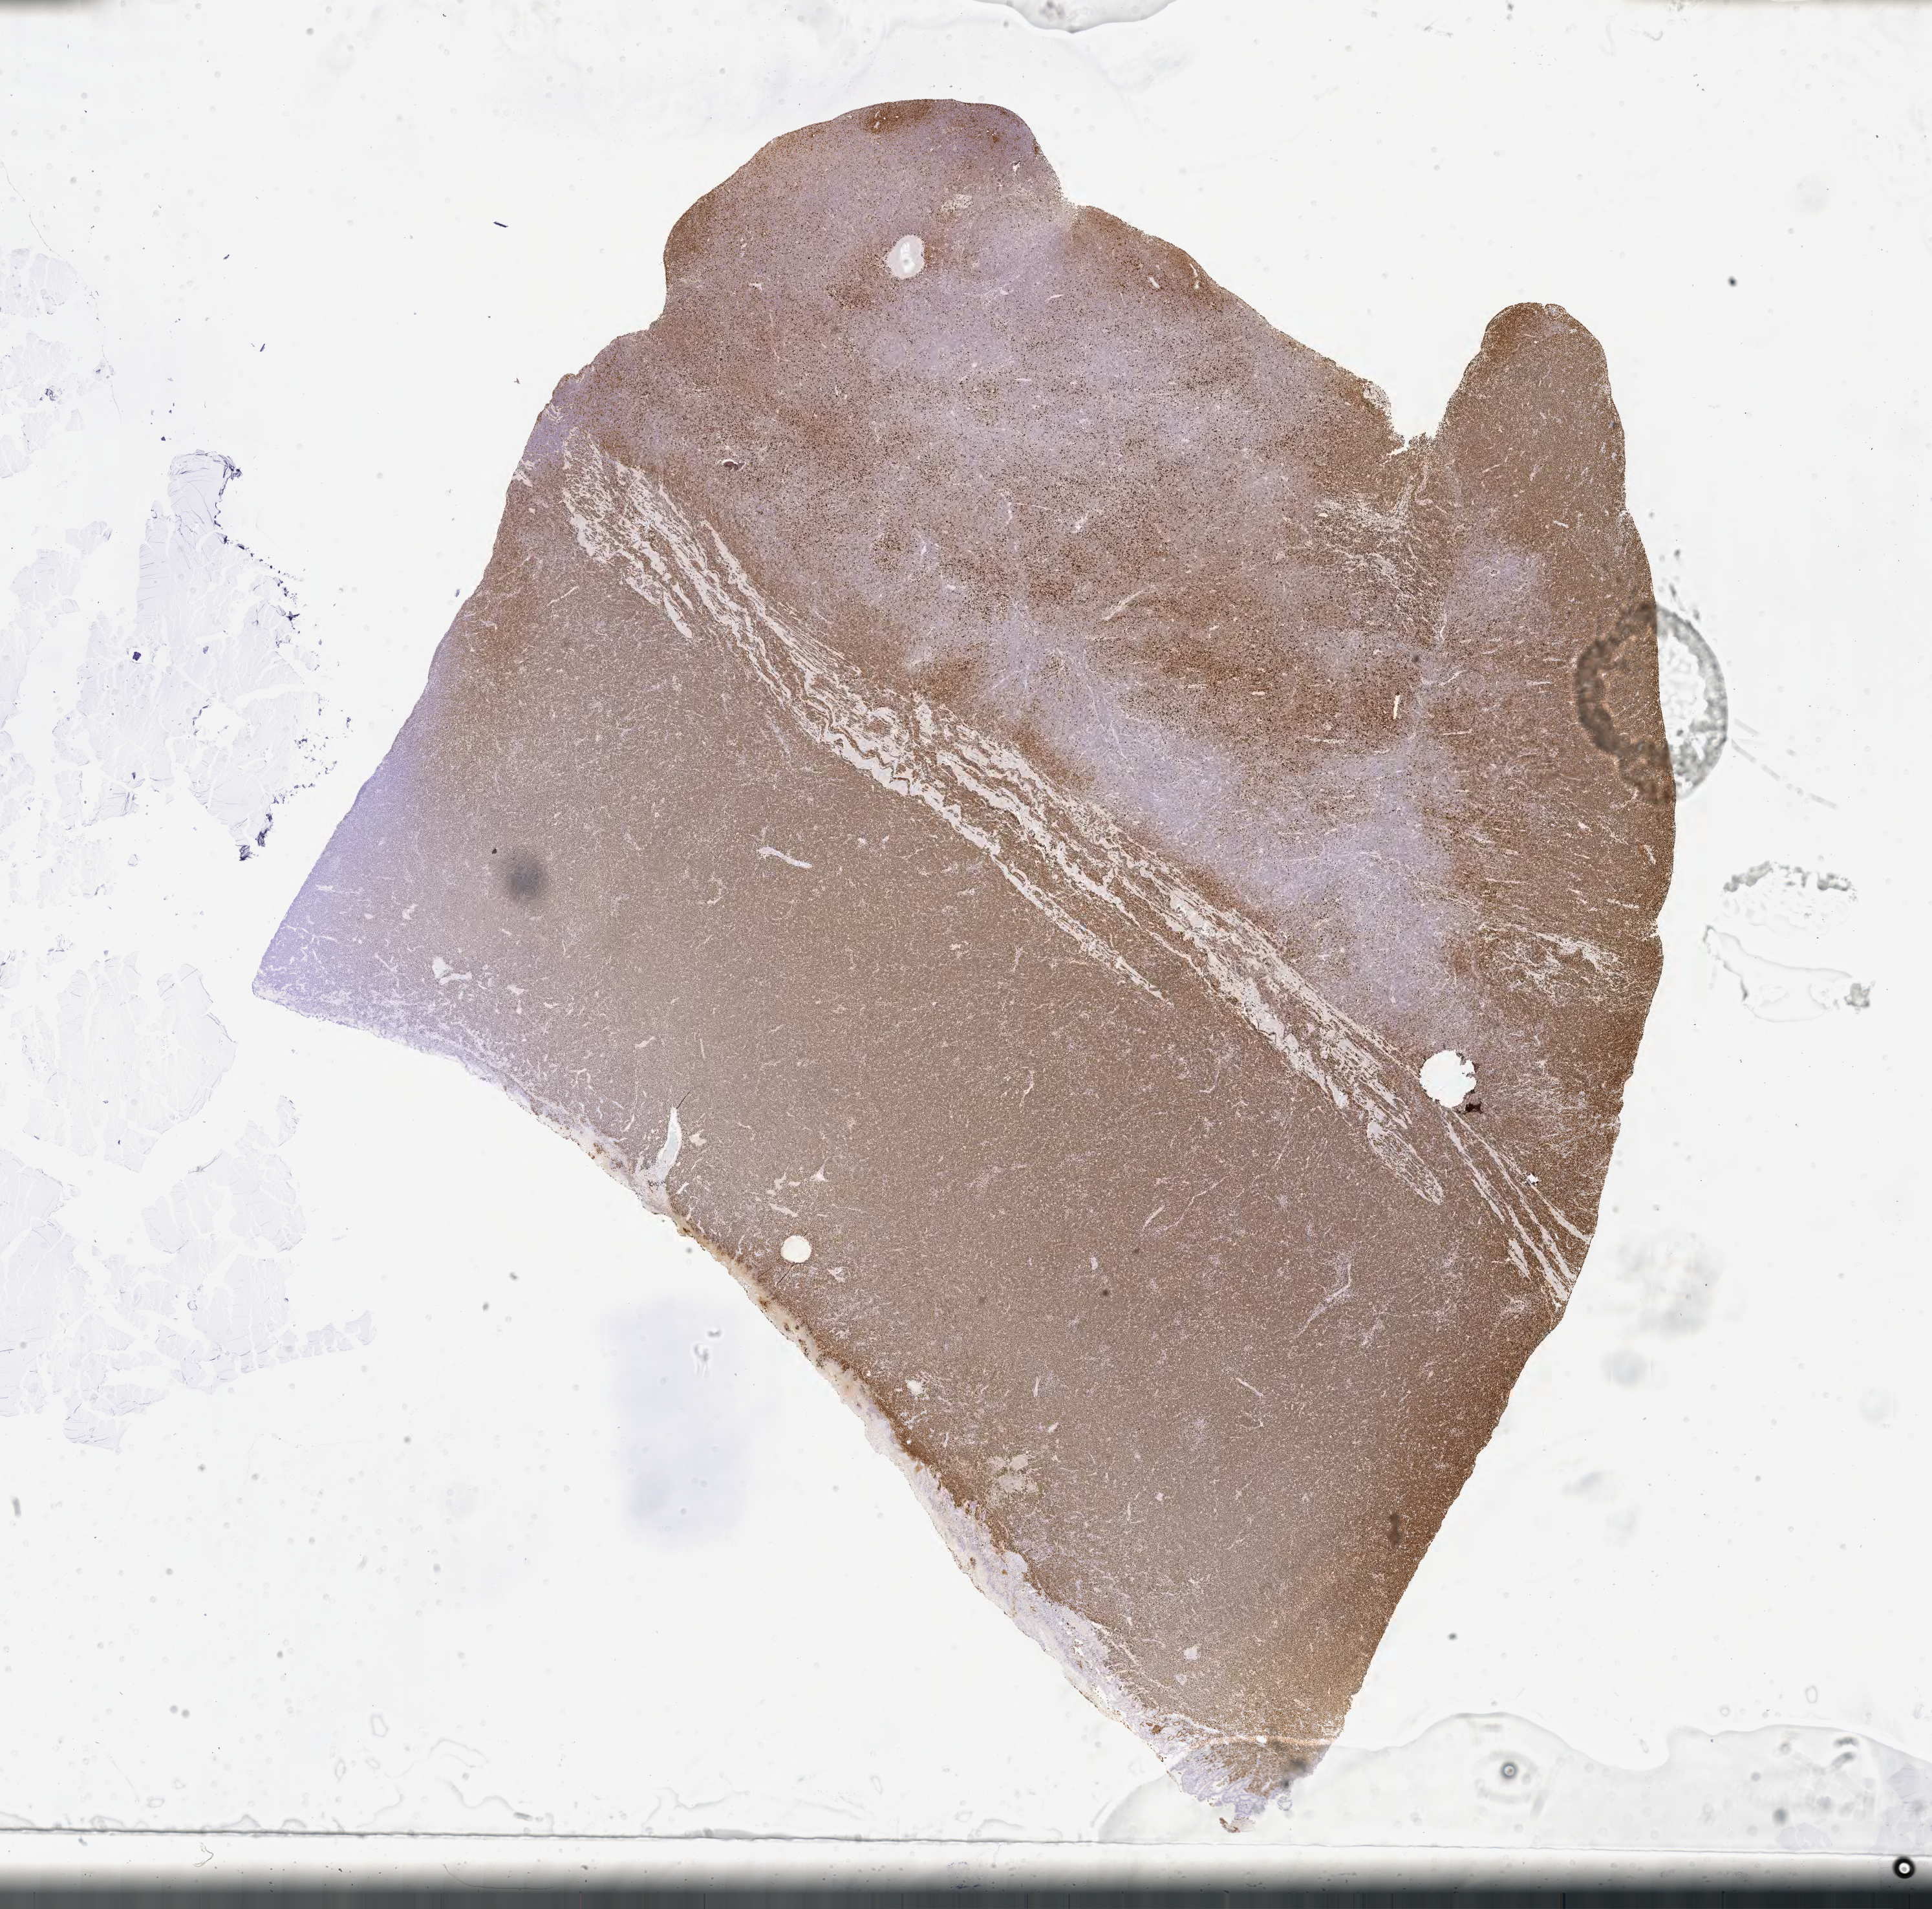
IHC for Ki-67, whole-slide image — a low-resolution overview of the entire scanned area, about 24.1 x 23.9 mm. Tumor tissue. Patient male; aged 36.
Diagnosis: Burkitt lymphoma, NOS.